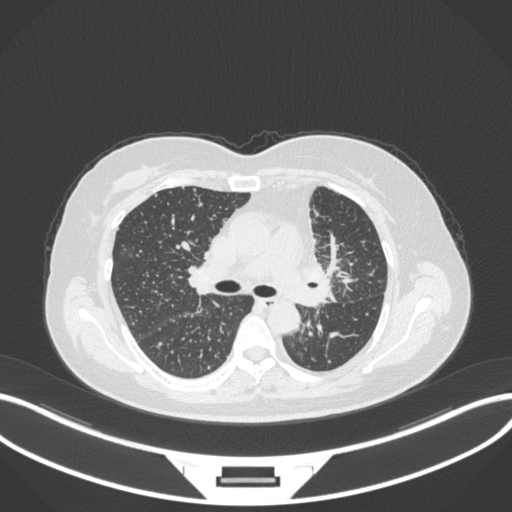
Chest CT, one axial slice; position 207 of 348 along the scan axis; reconstruction kernel B31f; 120 kVp; lung window (W 1500 / L -600 HU); 1 mm slice thickness; 512 × 512 image matrix, field of view 400 × 400 mm. Female patient, age 49 years. Case-level facts recorded for this patient, not image findings: clinical TNM (as recorded): T1c N0 M1.
Structures marked on this image (rectangle marked by the reading radiologist):
- lung tumour (recorded histology: adenocarcinoma): bounding box (x1, y1, x2, y2) in pixels: (294, 254, 340, 310)